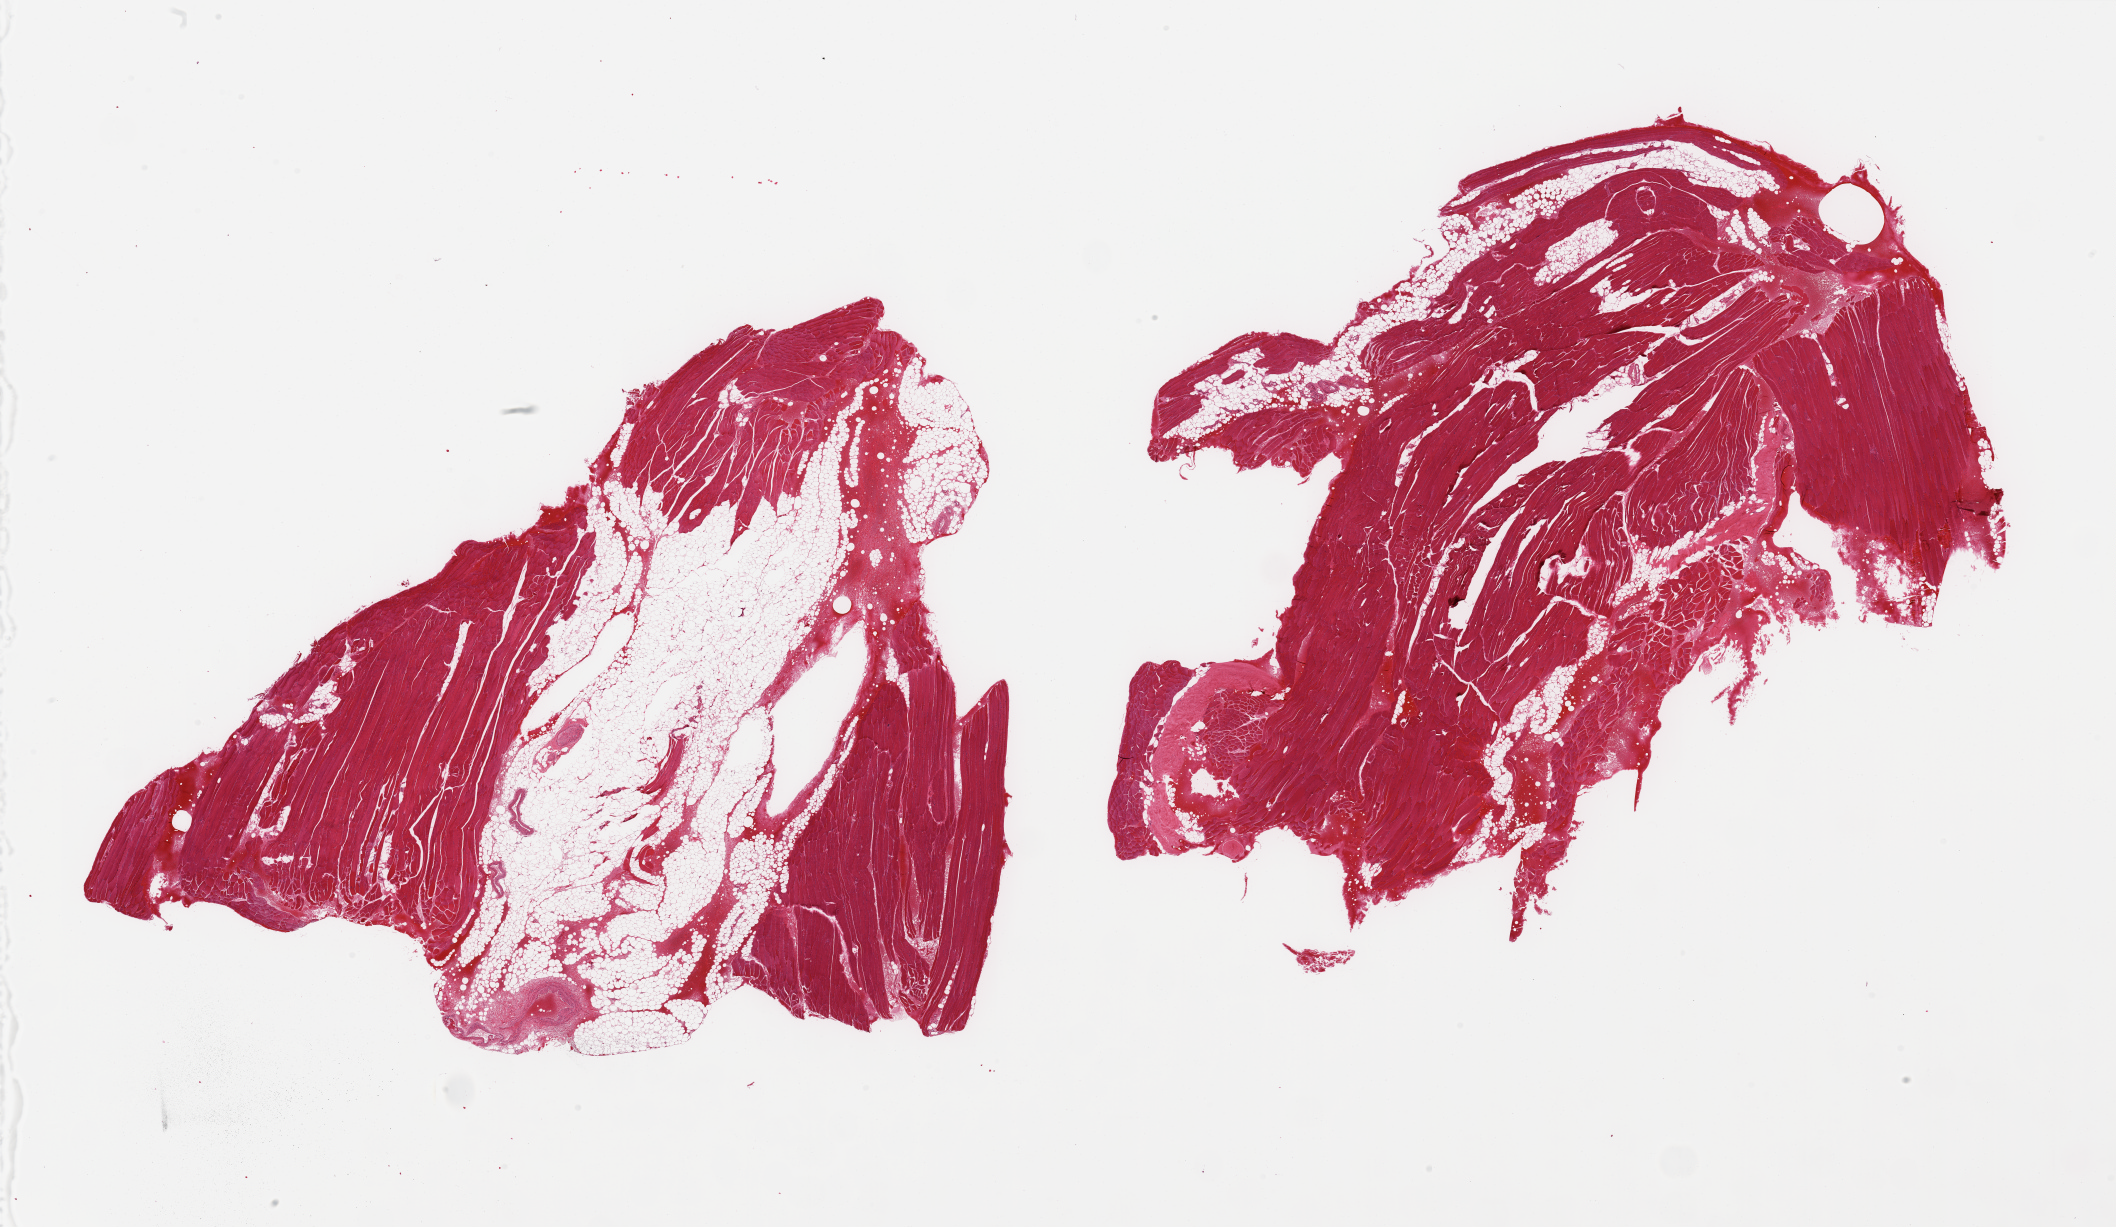
H&E whole-slide image, brightfield — whole scanned area (about 33.5 x 19.4 mm) shown as a low-resolution overview. PAXgene-fixed, paraffin-embedded tissue. Target tissue: skeletal muscle. Tissue donor sample. Donor: male.
Review note (as recorded): 2 pieces, ~30% interstitial fat.